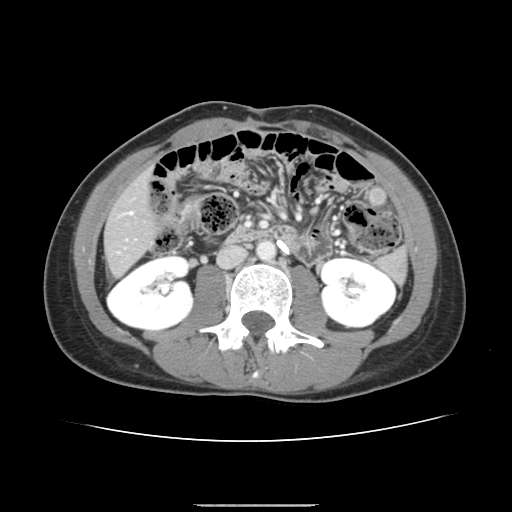
Contrast-enhanced abdominal CT, one axial slice; slice 47 of 150 in the series (ordered by position); intravenous contrast given; soft-tissue window (W 400 / L 40 HU); 2.5 mm slice thickness; 512 × 512 image matrix. Female patient, age 32 years. From the clinical record (not read from this slice): diagnosis: colorectal cancer liver metastases, imaged before liver resection; multiple liver metastases: yes; largest metastasis: 0.7 cm.
Outlined on this slice (expert manual segmentation):
- hepatic veins: bounding box <130,211,132,214> (left, top, right, bottom; pixels)
- liver: <106,176,154,274>
- planned liver remnant (the part of the liver to remain after resection): <106,177,154,274>